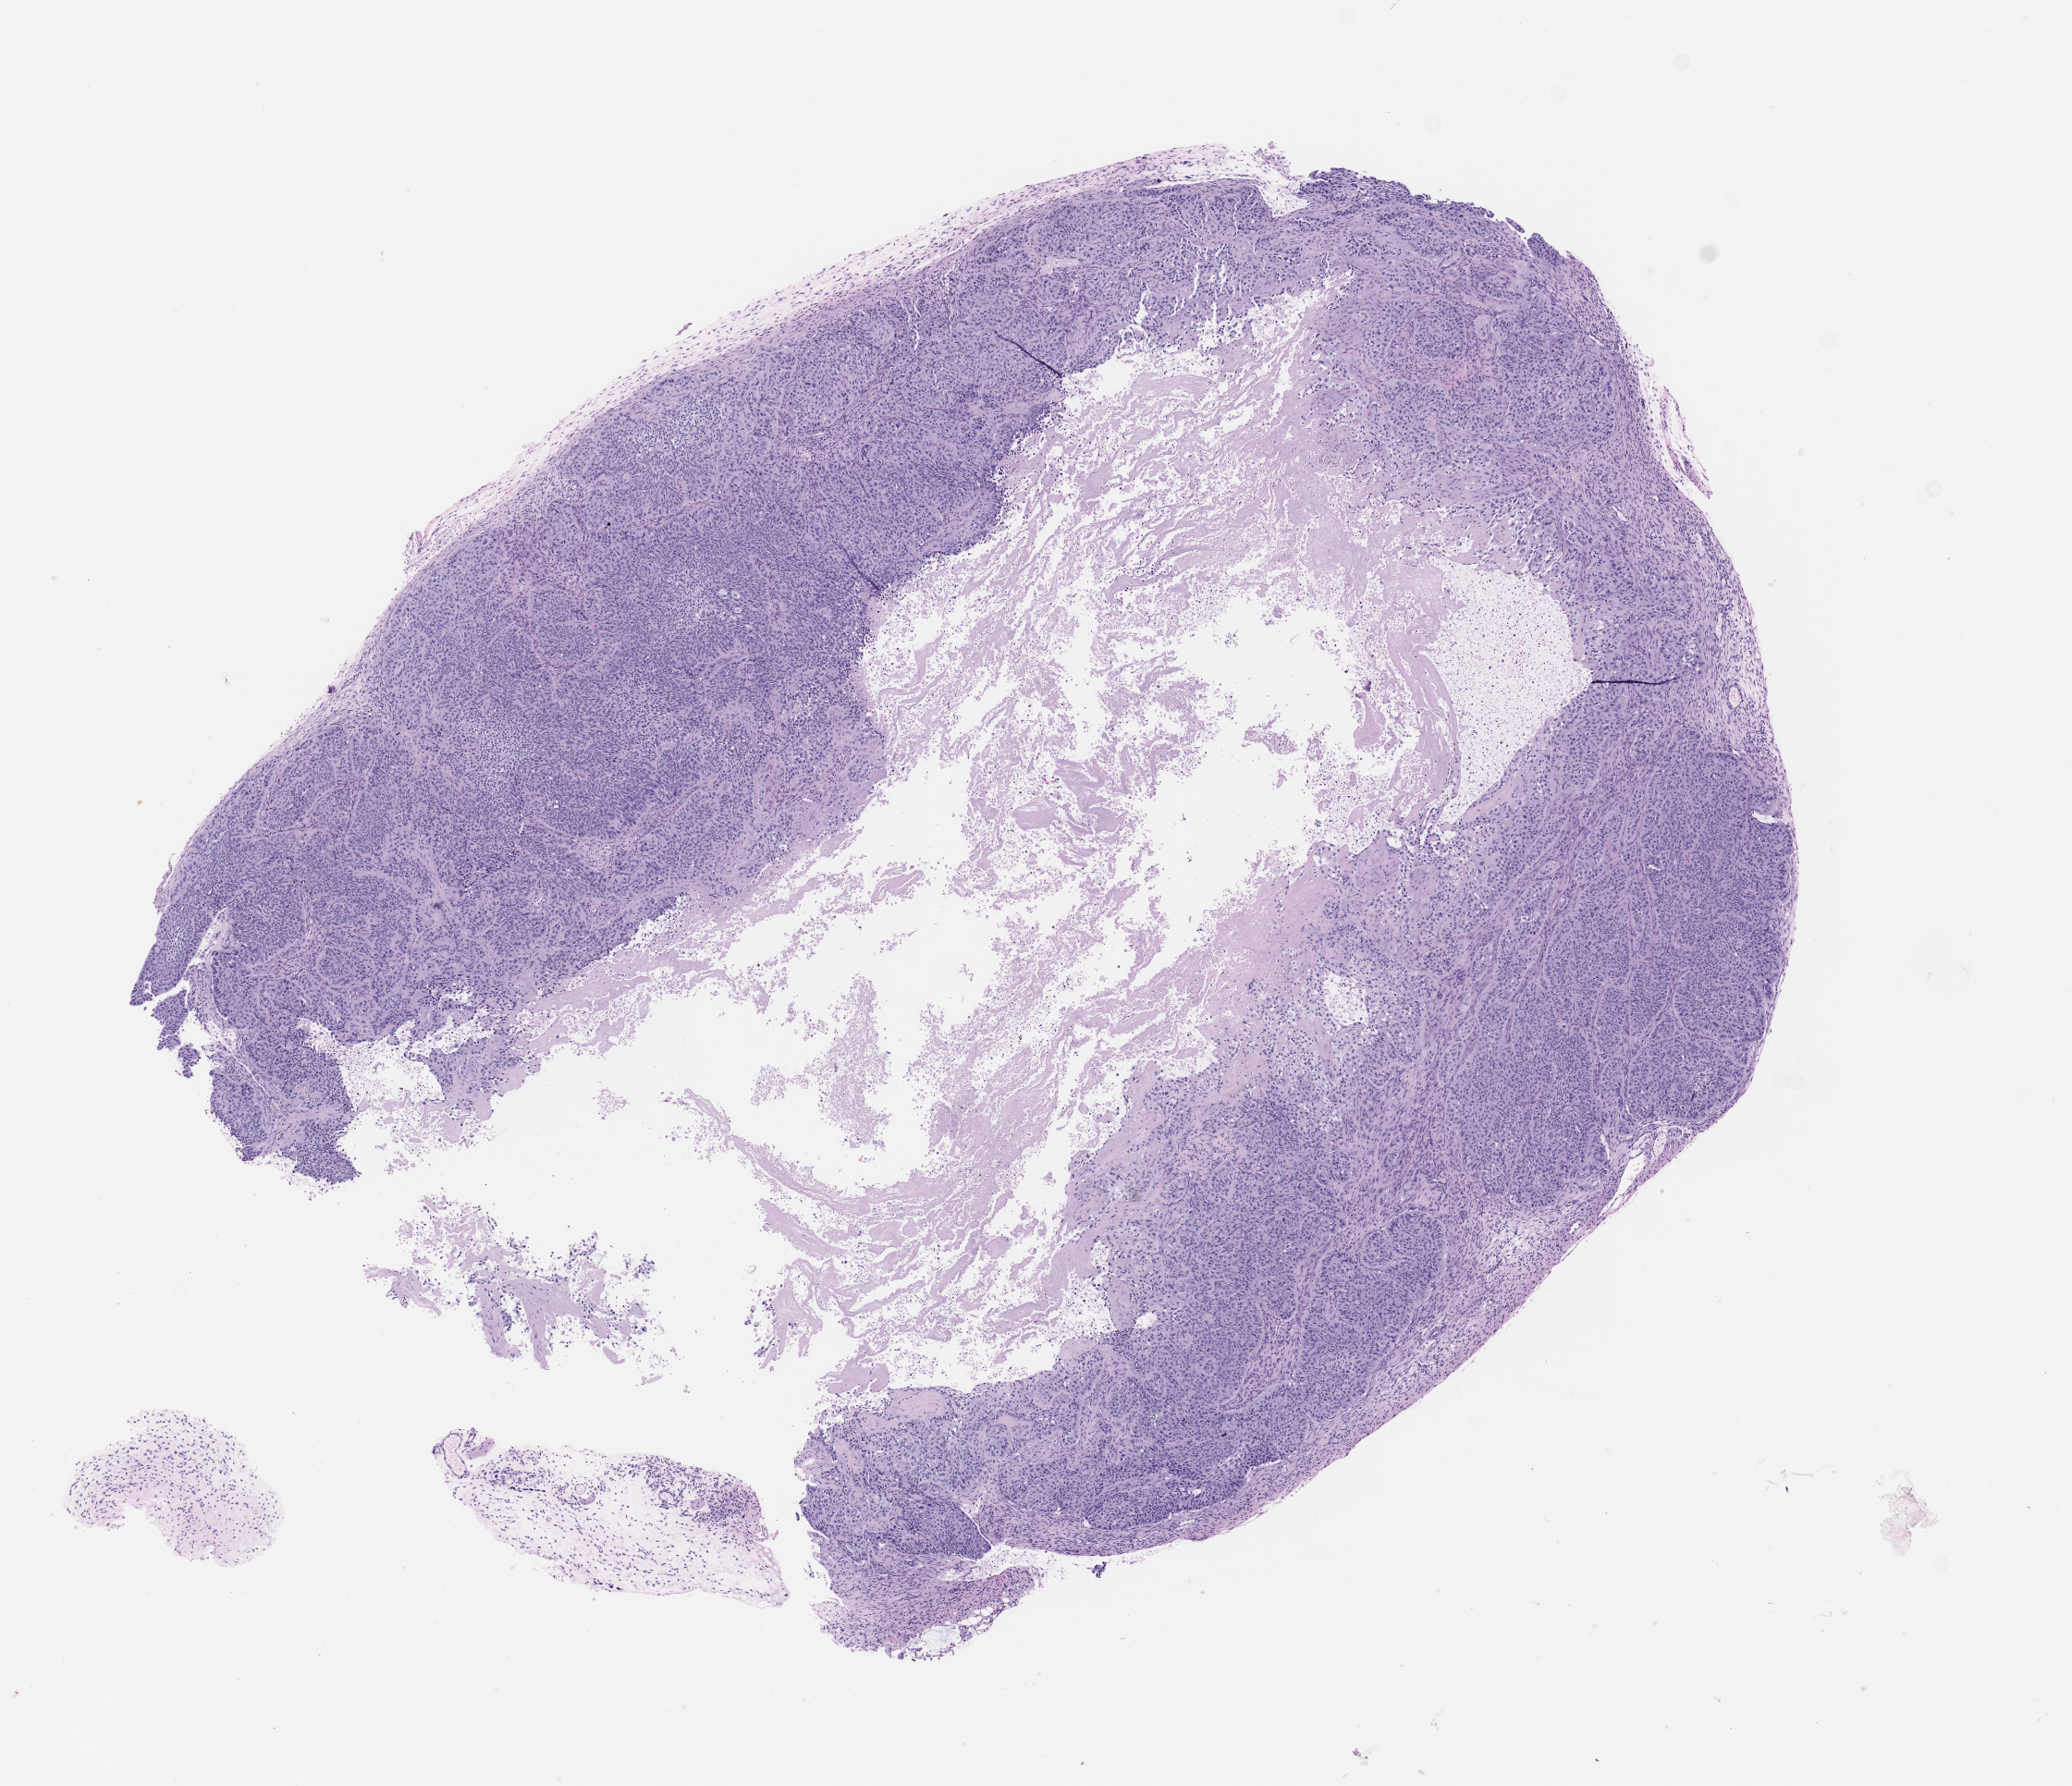
Whole-slide image, haematoxylin and eosin: patient-derived xenograft (human tumor grown in a mouse), passage 1, a low-resolution overview of the entire scanned area, about 9.0 x 7.8 mm, formalin-fixed, paraffin-embedded (FFPE) tissue, tumor site category: lung.
- originating patient diagnosis: Lung Squamous Cell Carcinoma